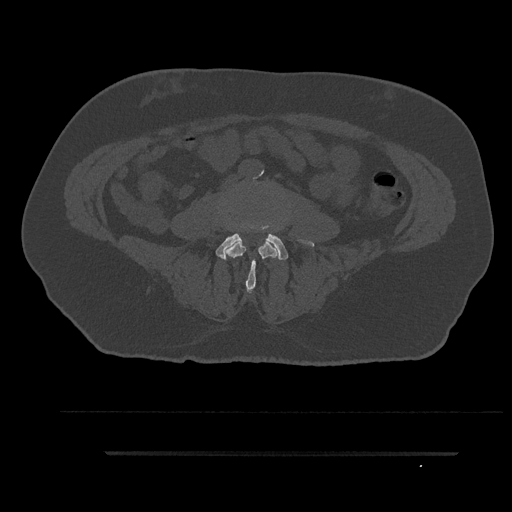
CT including the spine, one axial slice; slice 2 of 797 in the series (ordered by position); reconstruction kernel Br40s/3; 120 kVp; bone window (W 1800 / L 400 HU); 512 × 512 image matrix, field of view 432 × 432 mm. Patient: male, 63 years. Case-level facts recorded for this patient, not image findings: primary cancer: renal.
Outlined on this slice (semi-automatic segmentation, software-assisted and operator-edited):
- L3 vertebra: bounding box <225,240,278,291> (left, top, right, bottom; pixels)
- L4 vertebra: <216,234,288,260>